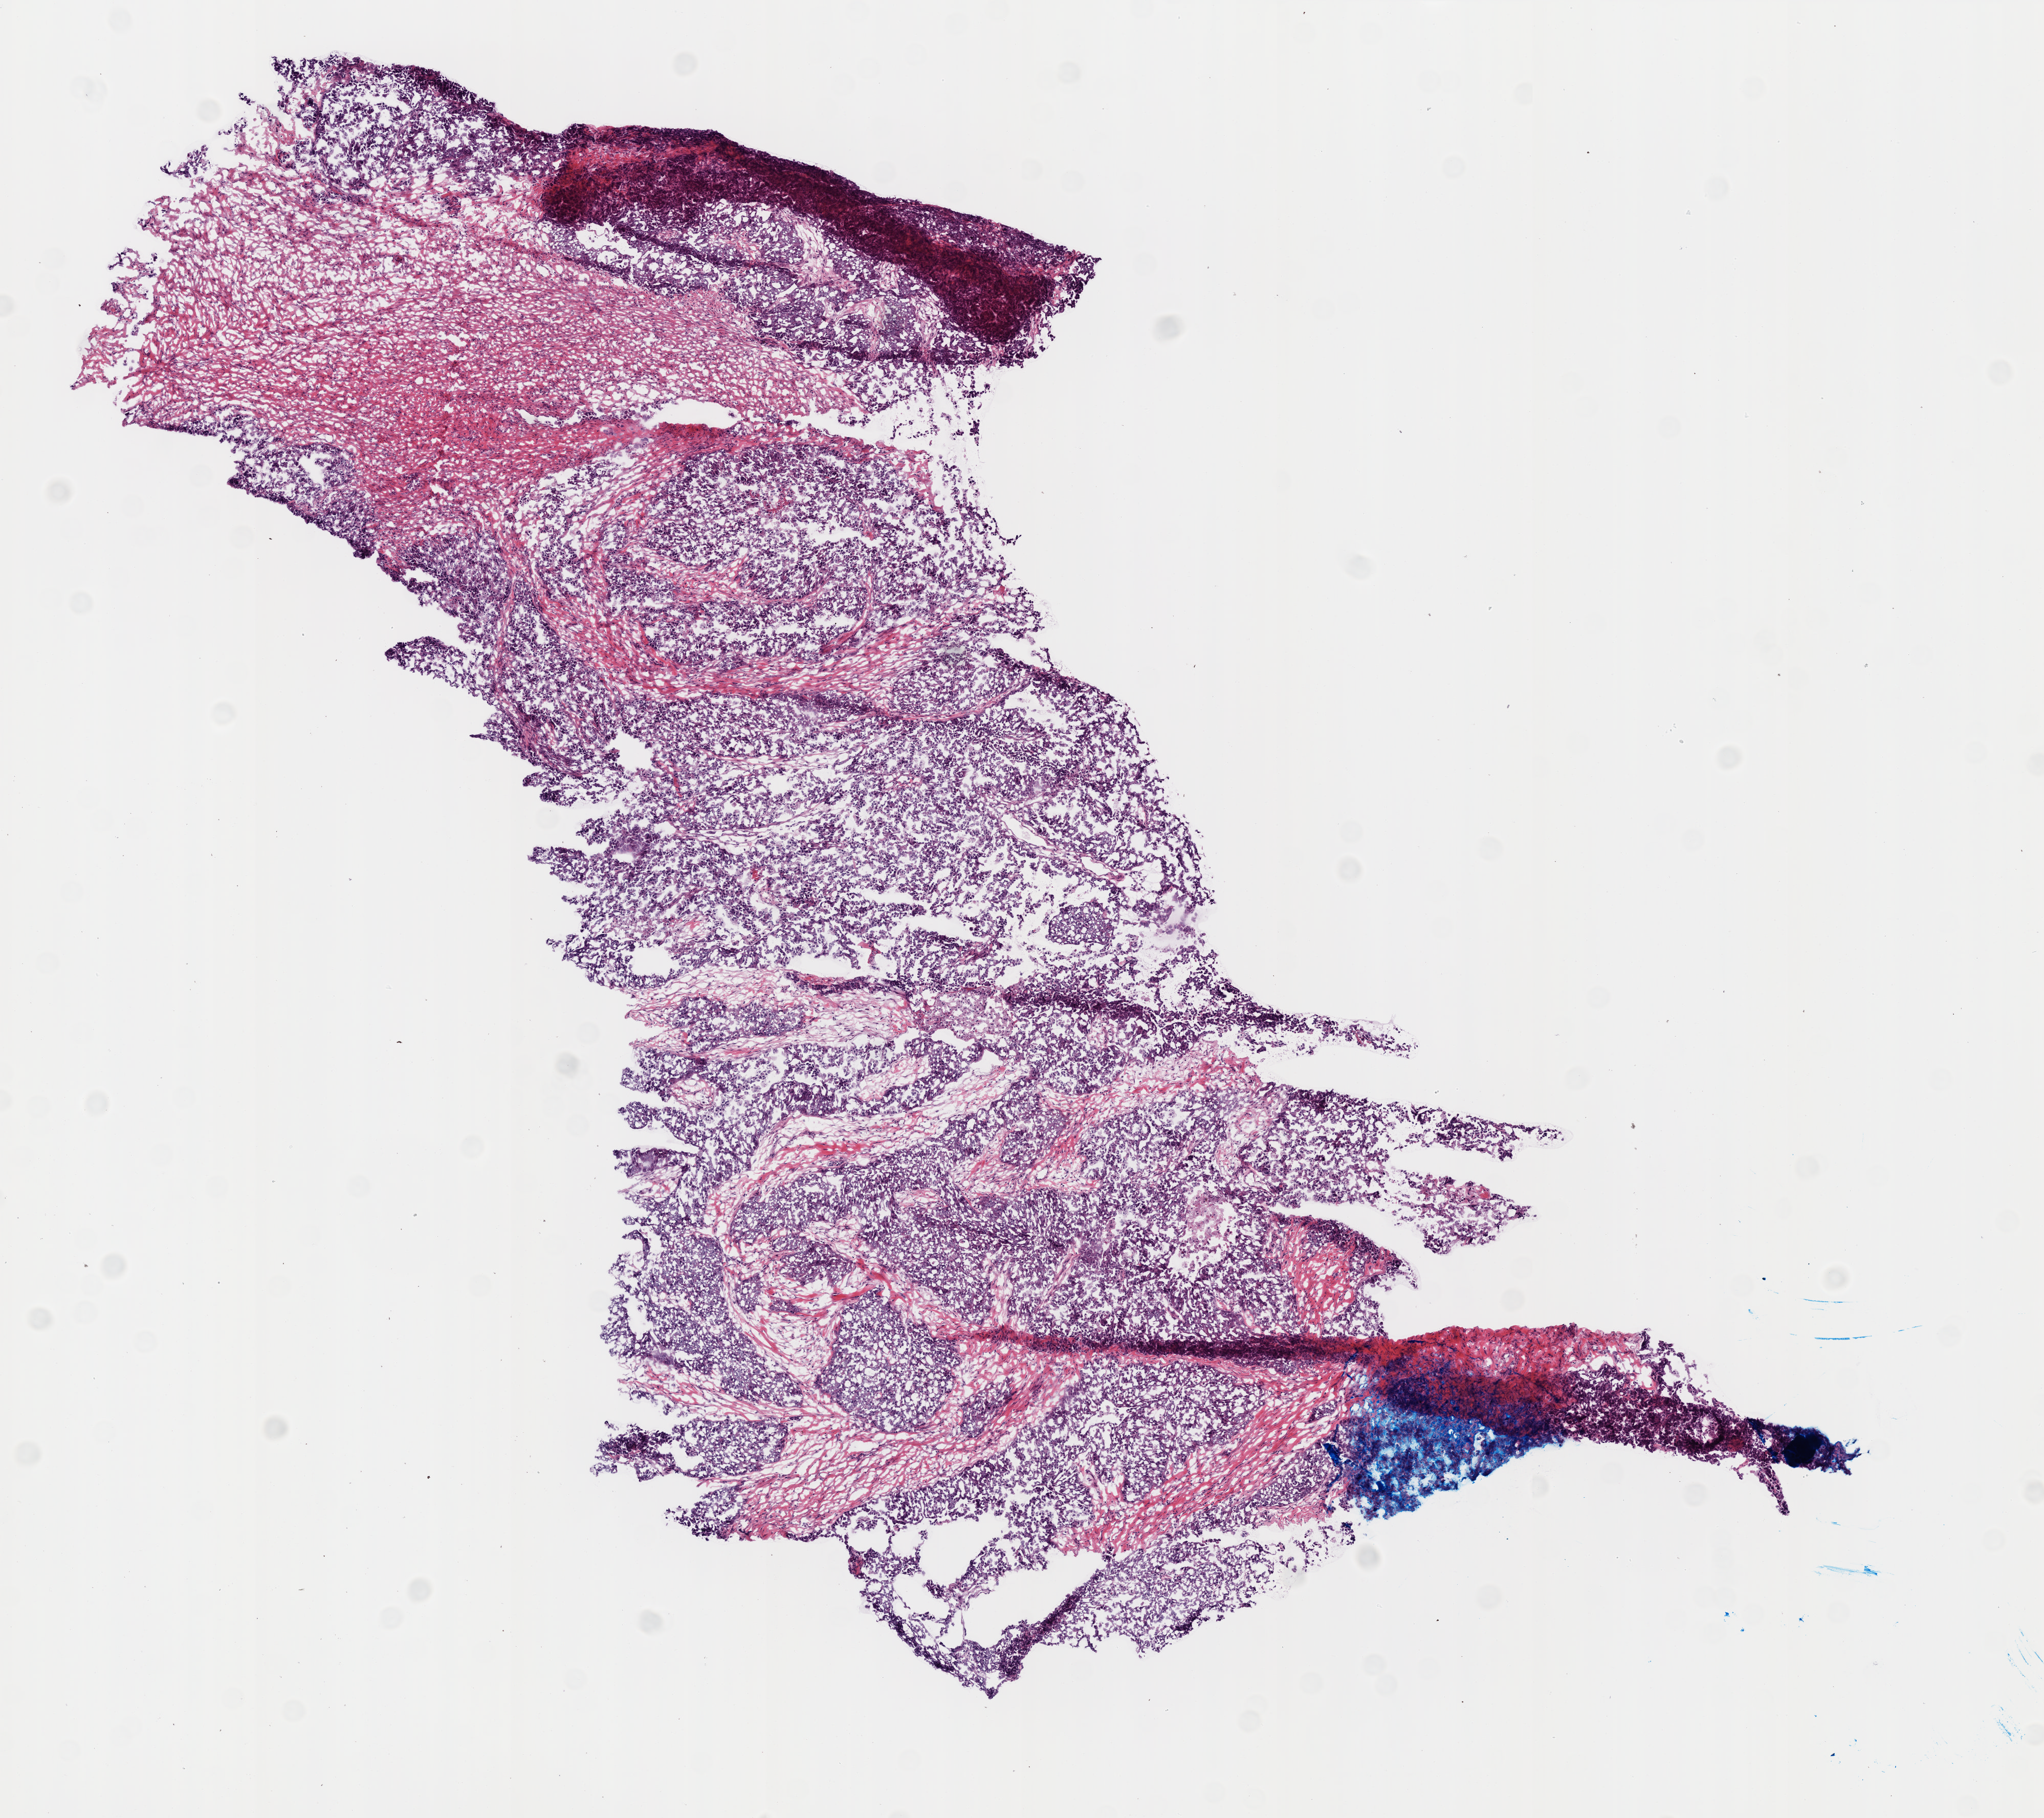
Whole-slide histology image, H&E-stained, a low-resolution overview of the entire scanned area, about 8.0 x 7.1 mm, frozen section, sample: primary tumour, ovary. Female patient; age at initial diagnosis 45 years. Histologic grade: G3 (poorly differentiated). Pathologist review of this section (percent, as recorded): tumour nuclei 90%, normal cells 0%, necrosis 0%.
Pathologic diagnosis: Serous cystadenocarcinoma, NOS. FIGO stage: IV.